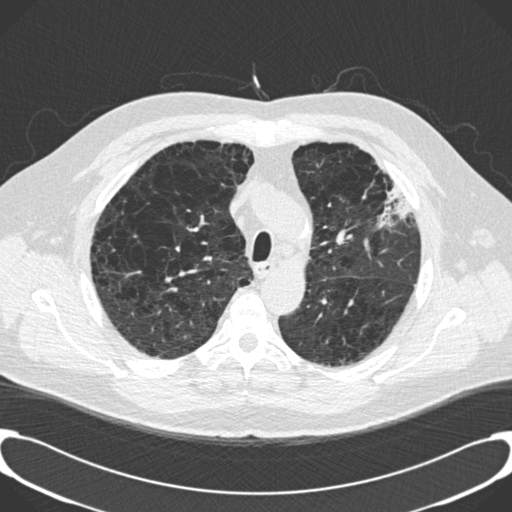
Axial slice from a low-dose chest CT screening exam; third annual screen; lung window (W 1500 / L -600 HU); 2 mm slice thickness; slice 44 of 189 in the series. Male, age 59 years at enrolment. Current smoker at enrolment.
Lesion marked by an expert reader, bounding box (x1, y1, x2, y2) in pixels: (360, 159, 416, 224). Screening reader's record for this exam: no non-calcified nodule ≥4 mm recorded. Official screen result: positive, other.